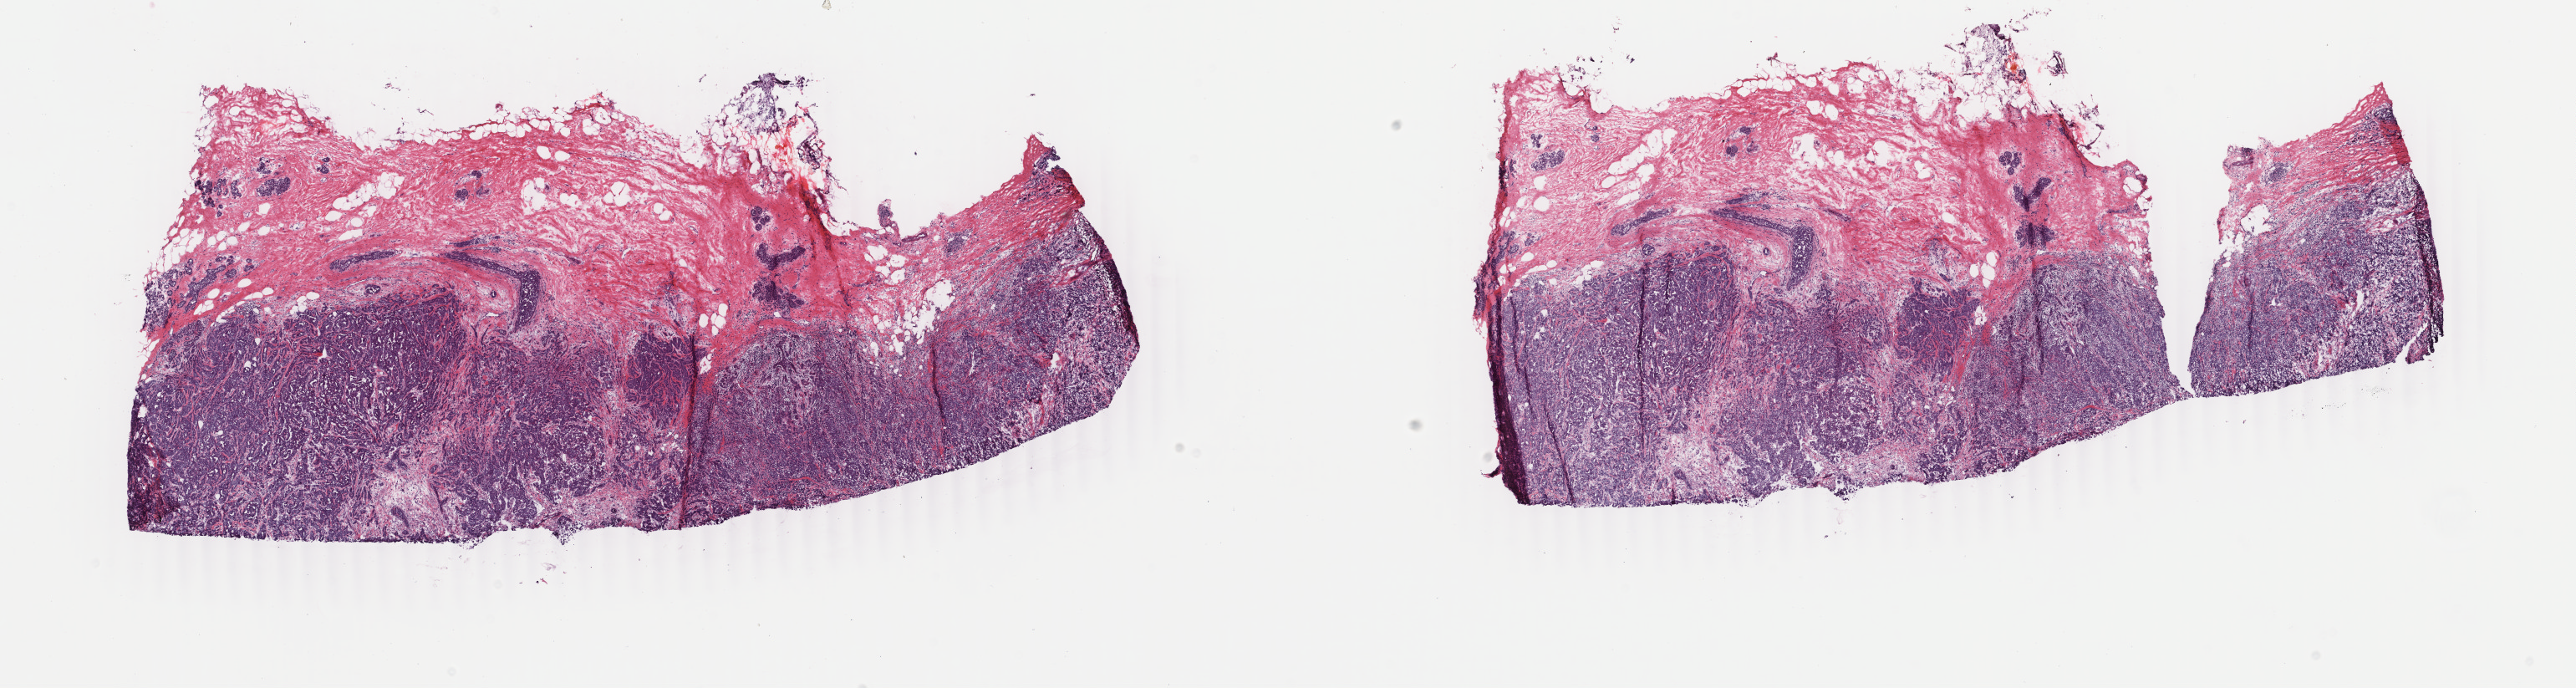
Digitized H&E tissue section (whole slide), whole scanned area (about 24.5 x 6.5 mm, acquisition: 40x scan) shown as a low-resolution overview, frozen section, breast, primary tumour sample. Patient: female, age at initial diagnosis 59 years. Composition of this section per pathologist review: tumour cells 70%, tumour nuclei 70%, normal cells 5%, stromal cells 24%, necrosis 1%. Inflammatory infiltration, as recorded: lymphocyte infiltration 3%, monocyte infiltration 1%, neutrophil infiltration 1%.
AJCC pathologic stage: IIB (6th edition). Lymph nodes positive (case pathology): 1 of 4 examined. Diagnosis: Infiltrating duct carcinoma, NOS.